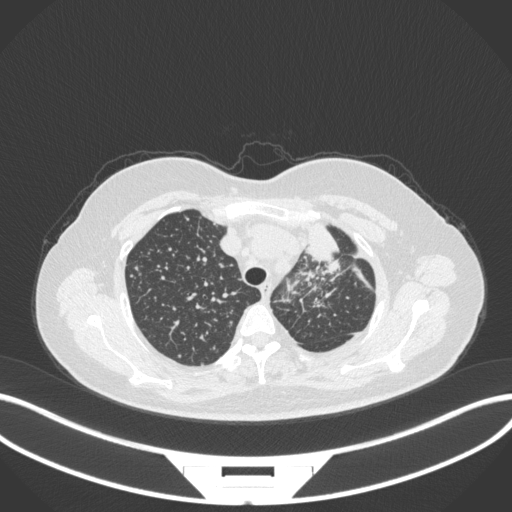
Chest CT, one axial slice; reconstruction kernel B31f; 120 kVp; lung window (W 1500 / L -600 HU); 1 mm slice thickness; 512 × 512 image matrix, field of view 400 × 400 mm. Female patient, age 49 years. Case-level facts recorded for this patient, not image findings: clinical TNM (as recorded): T1c N0 M1.
Annotated regions visible in this slice (bounding box drawn by a radiologist):
- lung tumour (recorded histology: adenocarcinoma): bounding box <302,216,343,266> (left, top, right, bottom; pixels)